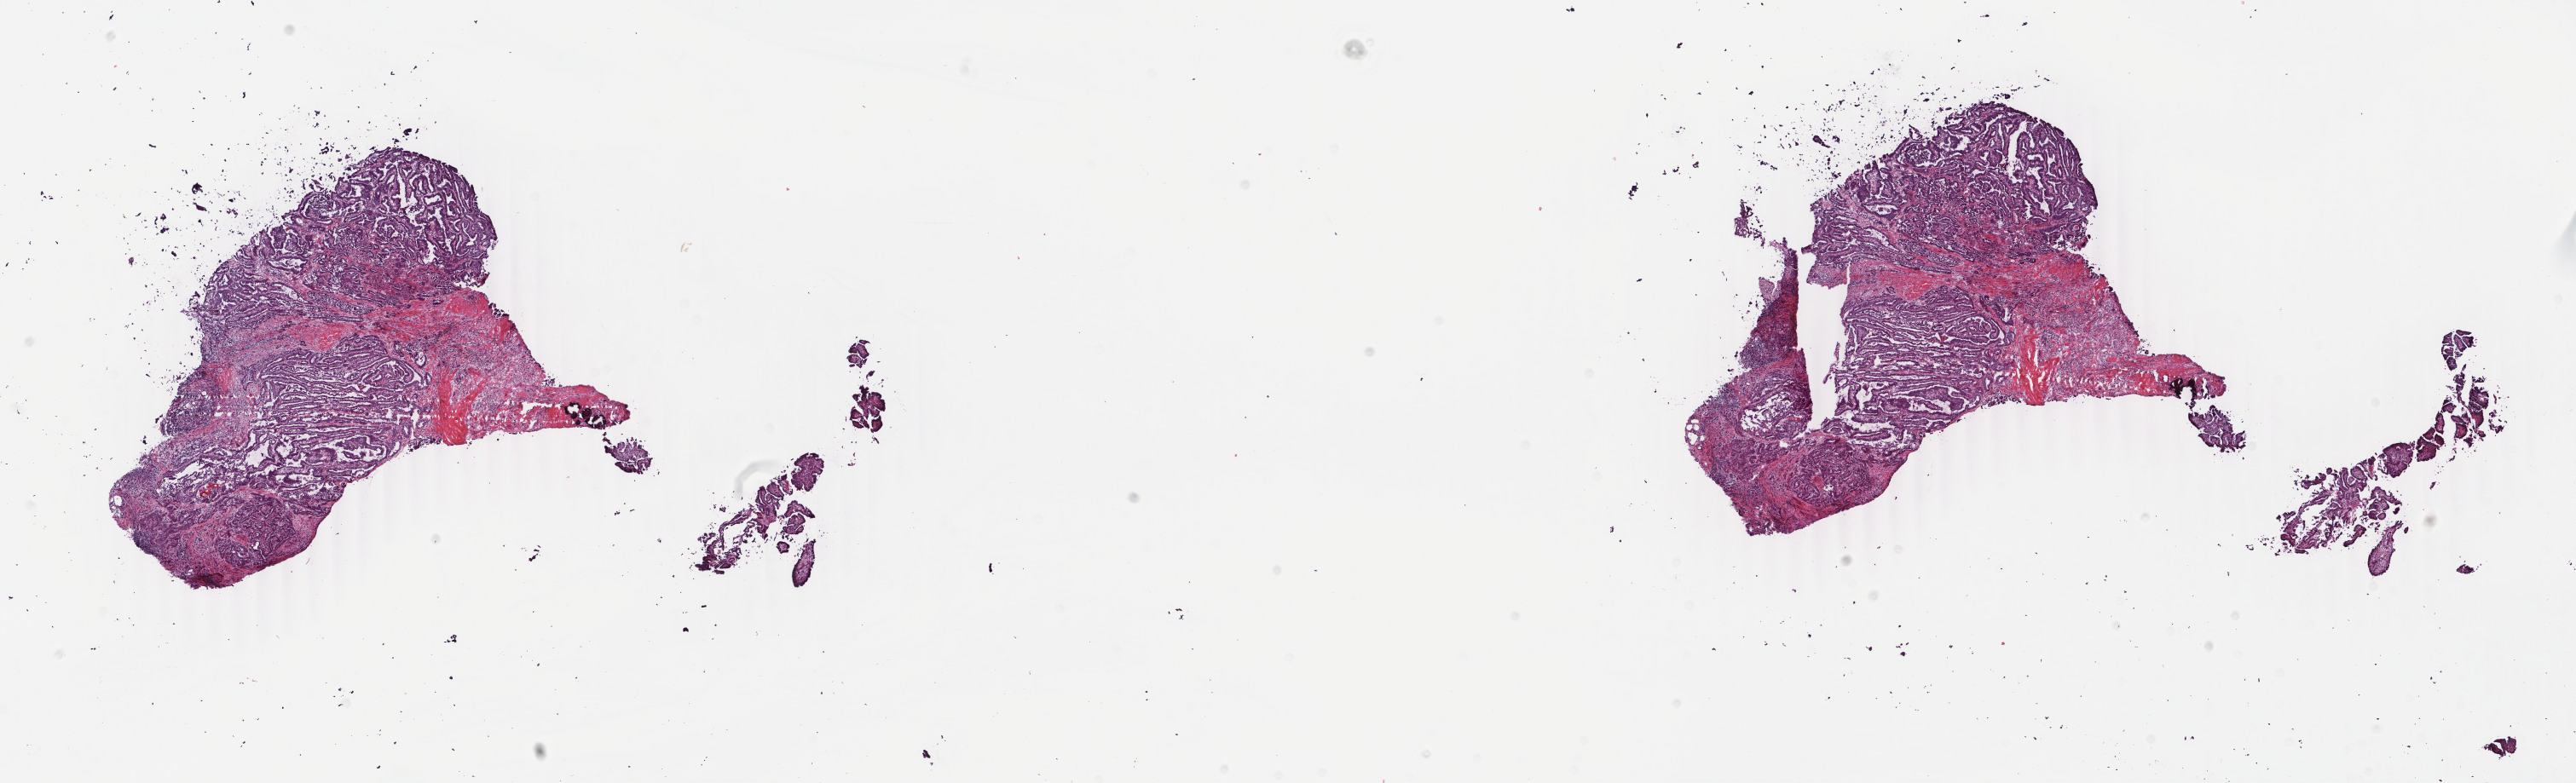
Whole-slide histology image, H&E — shown as a low-resolution overview of the whole scanned area (about 24.0 x 7.3 mm), frozen section from the bottom of the tissue portion, thyroid, primary tumour sample. Male, age 85 years at initial diagnosis. Slide review estimates, as recorded: tumour cells 80%, tumour nuclei 65%, normal cells 0%, stromal cells 20%, necrosis 0%. Infiltration values recorded for this section: lymphocyte infiltration 0%, monocyte infiltration 0%, neutrophil infiltration 0%.
Laterality: right. Pathologic diagnosis: Papillary carcinoma, columnar cell (thyroid gland). AJCC pathologic stage: I (7th edition).